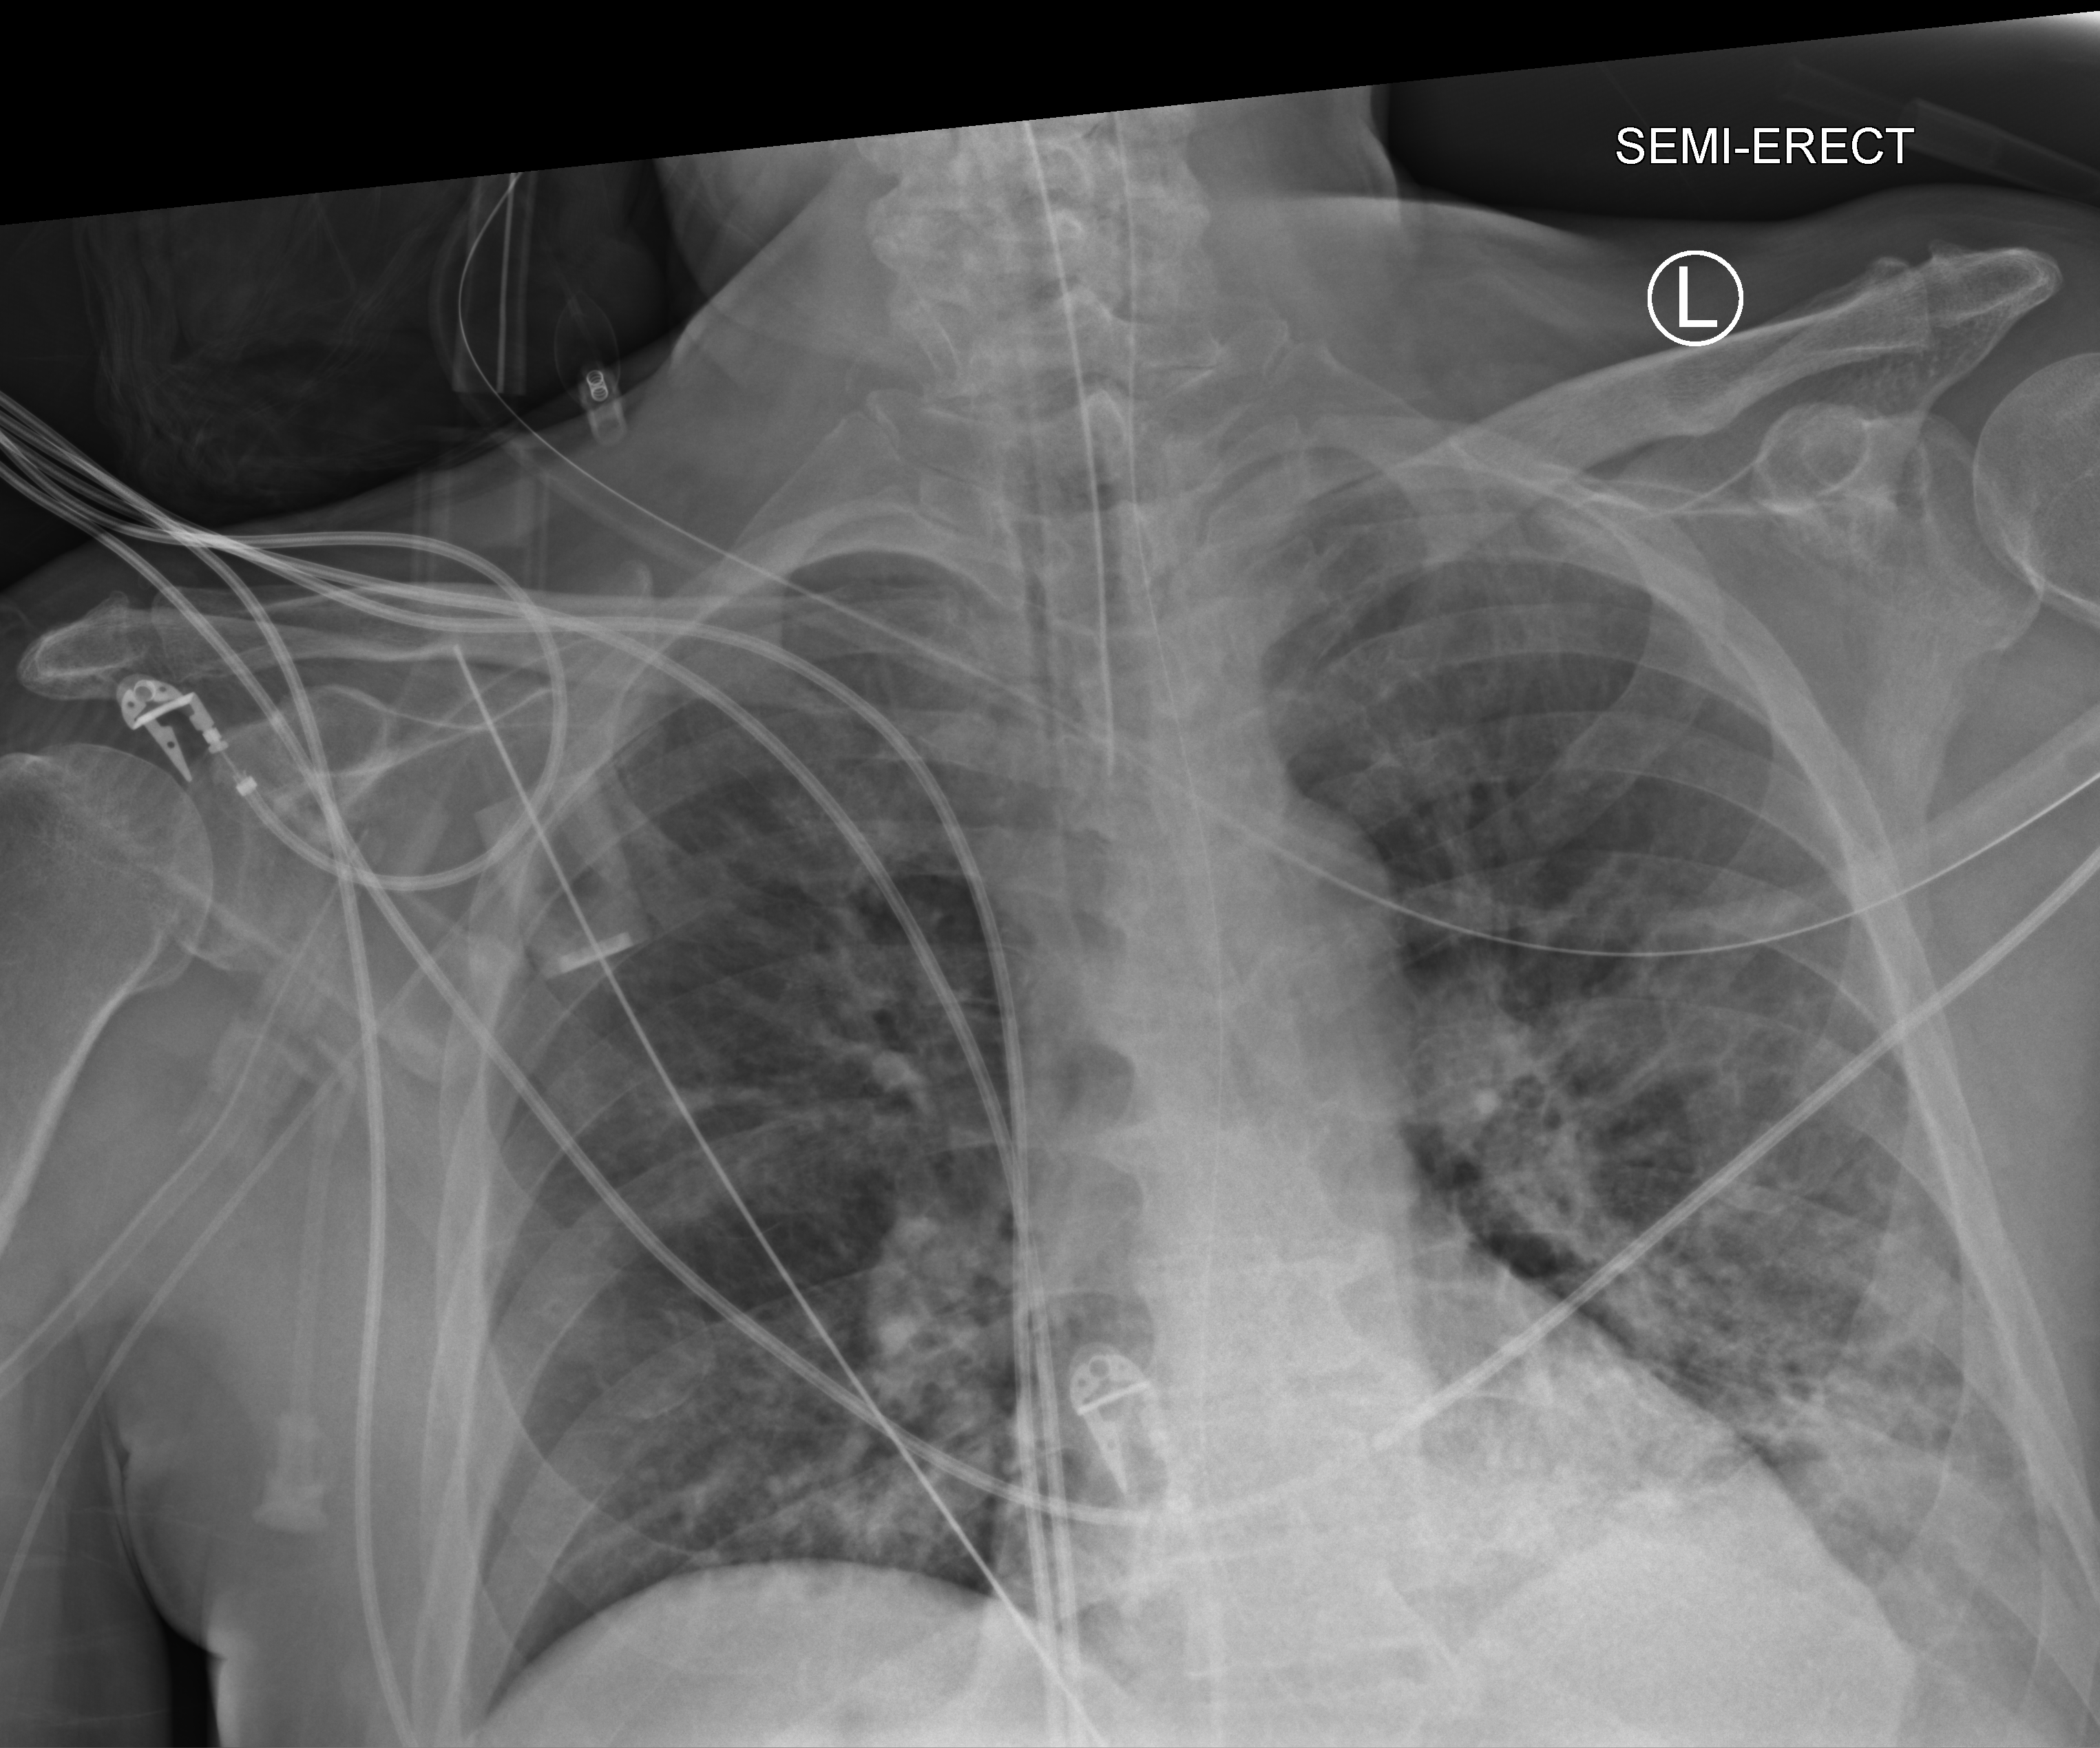
Portable chest radiograph; anteroposterior (AP) projection. Male patient hospitalised with COVID-19, age 60–74 years.
Admission-level facts for this patient (not findings on this image; timing relative to this image not recorded):
- admitted to intensive care during this hospital stay: yes
- mechanically ventilated during this hospital stay: yes